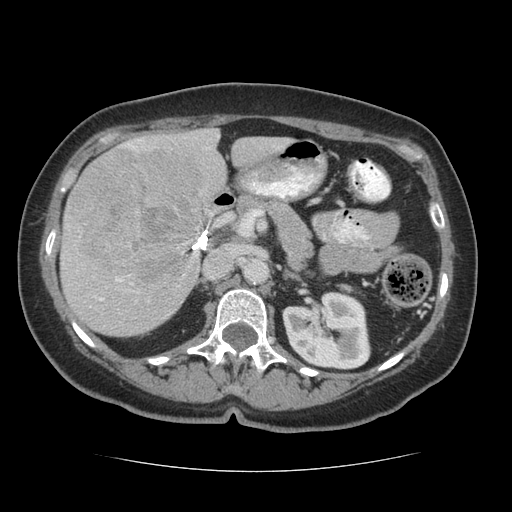
Contrast-enhanced abdominal CT (liver protocol), one axial slice. Slice 30 of 75 in the series (ordered by position). Soft-tissue window (W 400 / L 40 HU). 512 × 512 image matrix. From the clinical record (not read from this slice): diagnosis: hepatocellular carcinoma (patient treated with transarterial chemoembolisation; whether this scan precedes or follows treatment is not stated here); TNM stage (as recorded): Stage-I; Child-Pugh class: A; tumour nodularity: uninodular.
Outlined on this slice (semi-automatically segmented with operator editing):
- liver parenchyma outside the tumour (the mass and vessels are separate outlines, so this box may not span the whole liver): box from (x=60, y=128) to (x=291, y=336) px
- mass: (x=67, y=148)–(x=207, y=286)
- liver vessels: (x=68, y=135)–(x=279, y=301)